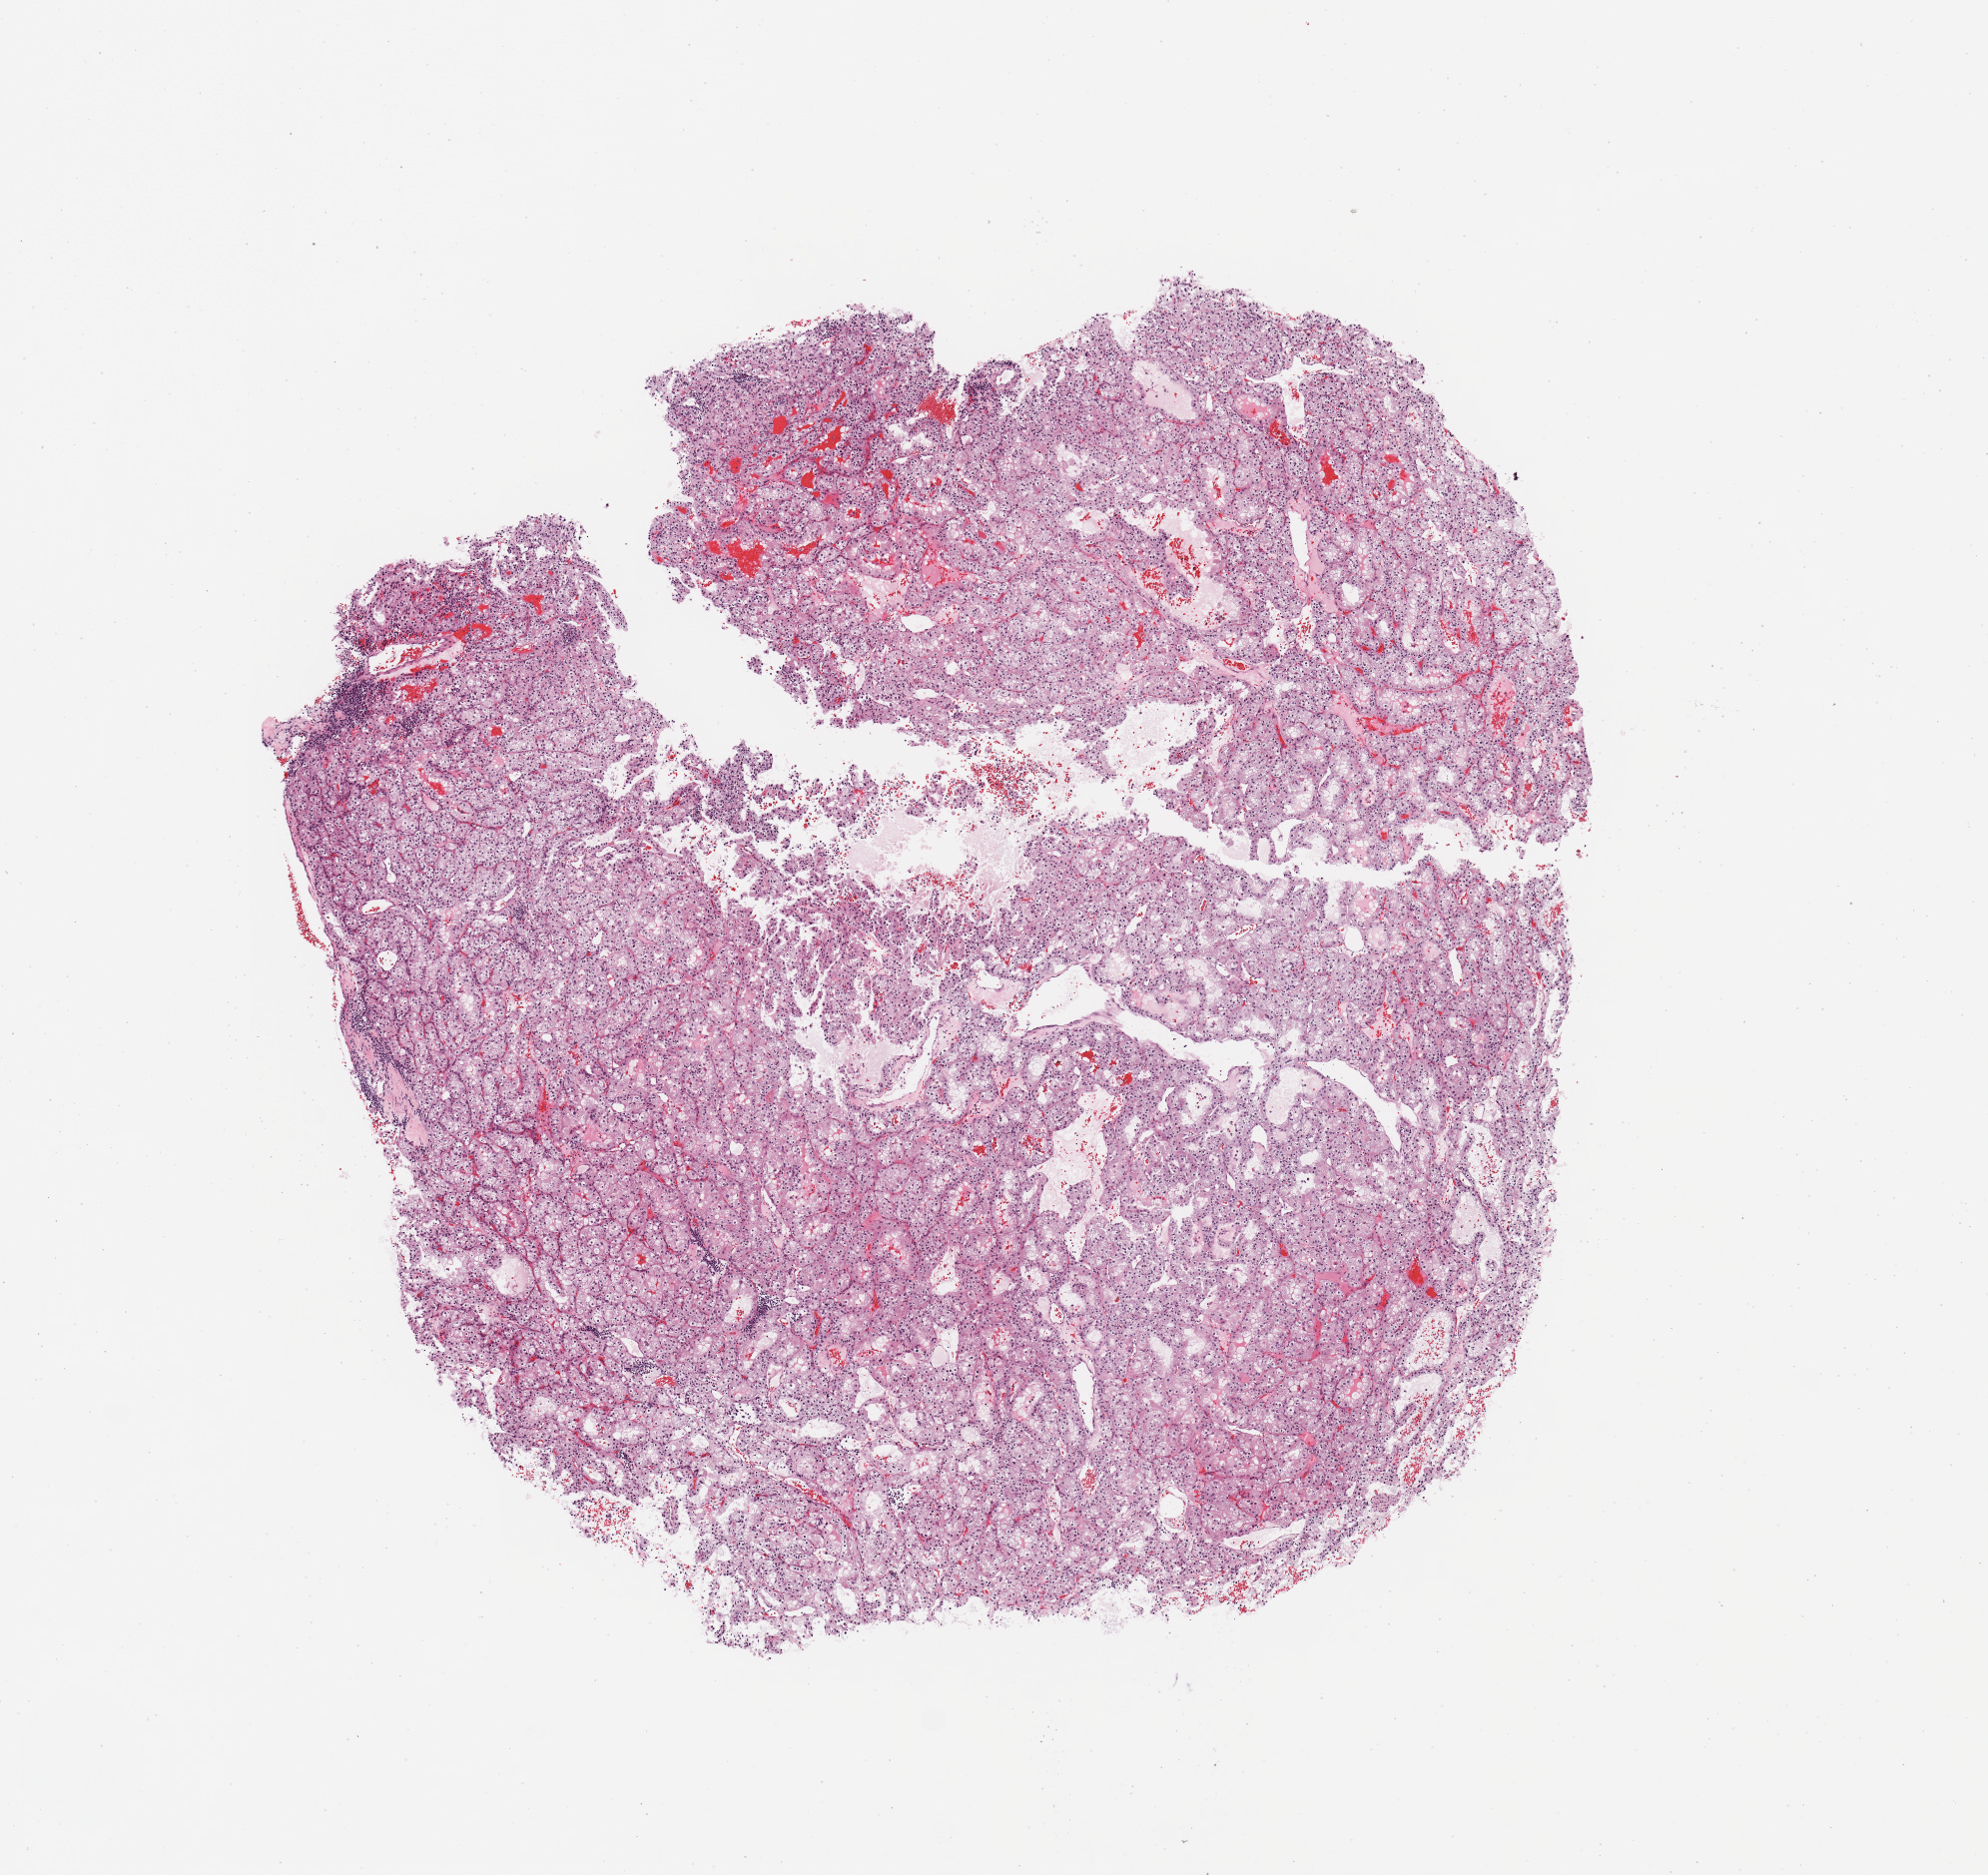
Digitized Hematoxylin and eosin (H&E) stained tissue section (whole slide), low-resolution overview of the scanned area, about 7.9 x 7.4 mm (acquisition: 20x scan); tumour tissue sample, sampled site: kidney. Patient: male, age 72 years. Histologic grade: G3 (poorly differentiated). Slide review estimates, as recorded: tumour nuclei 90%, necrosis 0%.
Histologic diagnosis: Renal cell carcinoma, NOS. AJCC pathologic stage: II.